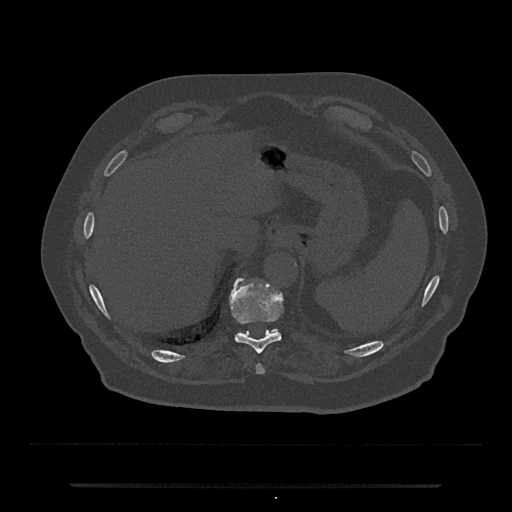
CT including the spine, one axial slice. Slice 697 of 797 in the series (ordered by position). 120 kVp. Bone window (W 1800 / L 400 HU). 512 × 512 image matrix, field of view 434 × 434 mm. Patient: male, 80 years. From the clinical record (not read from this slice): primary cancer: prostate; vertebrae with lytic lesions (as recorded): L1, T11.
Outlined on this slice (semi-automatic segmentation, software-assisted and operator-edited):
- T10 vertebra: box from (x=229, y=278) to (x=283, y=354) px
- T11 vertebra: (x=271, y=328)–(x=279, y=333)
- T9 vertebra: (x=256, y=364)–(x=264, y=374)